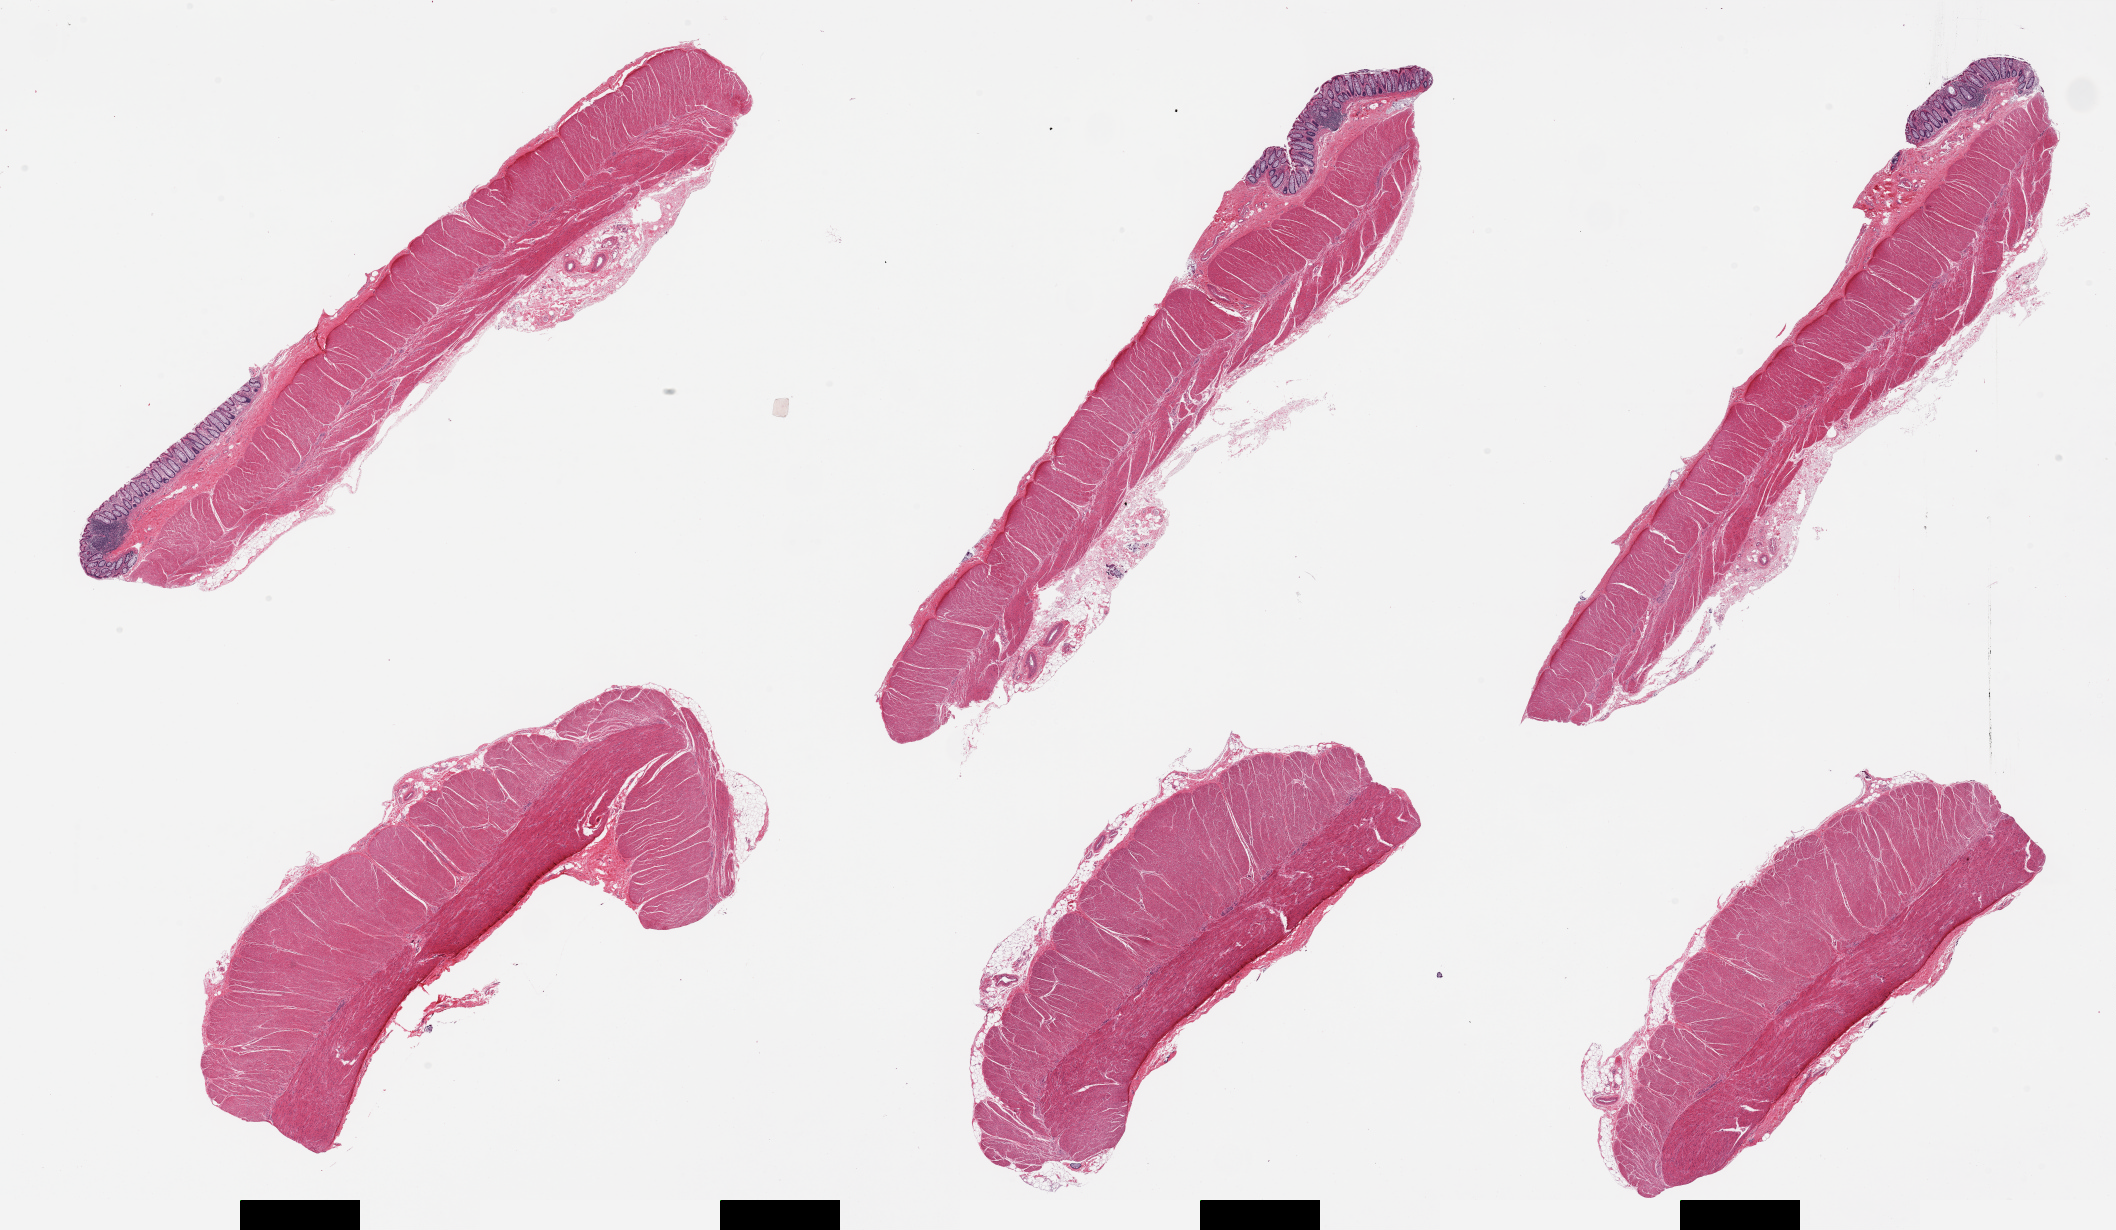
Digitized hematoxylin and eosin (H&E)-stained section, brightfield — a low-resolution overview of the entire scanned area, about 33.5 x 19.5 mm (from a 20x scan), PAXgene-fixed paraffin-embedded (PFPE) section, section of sigmoid colon (target tissue), tissue donor sample. Female donor.
- review note (as recorded): 6 pieces. 3 have foci of mucosa (not the target)